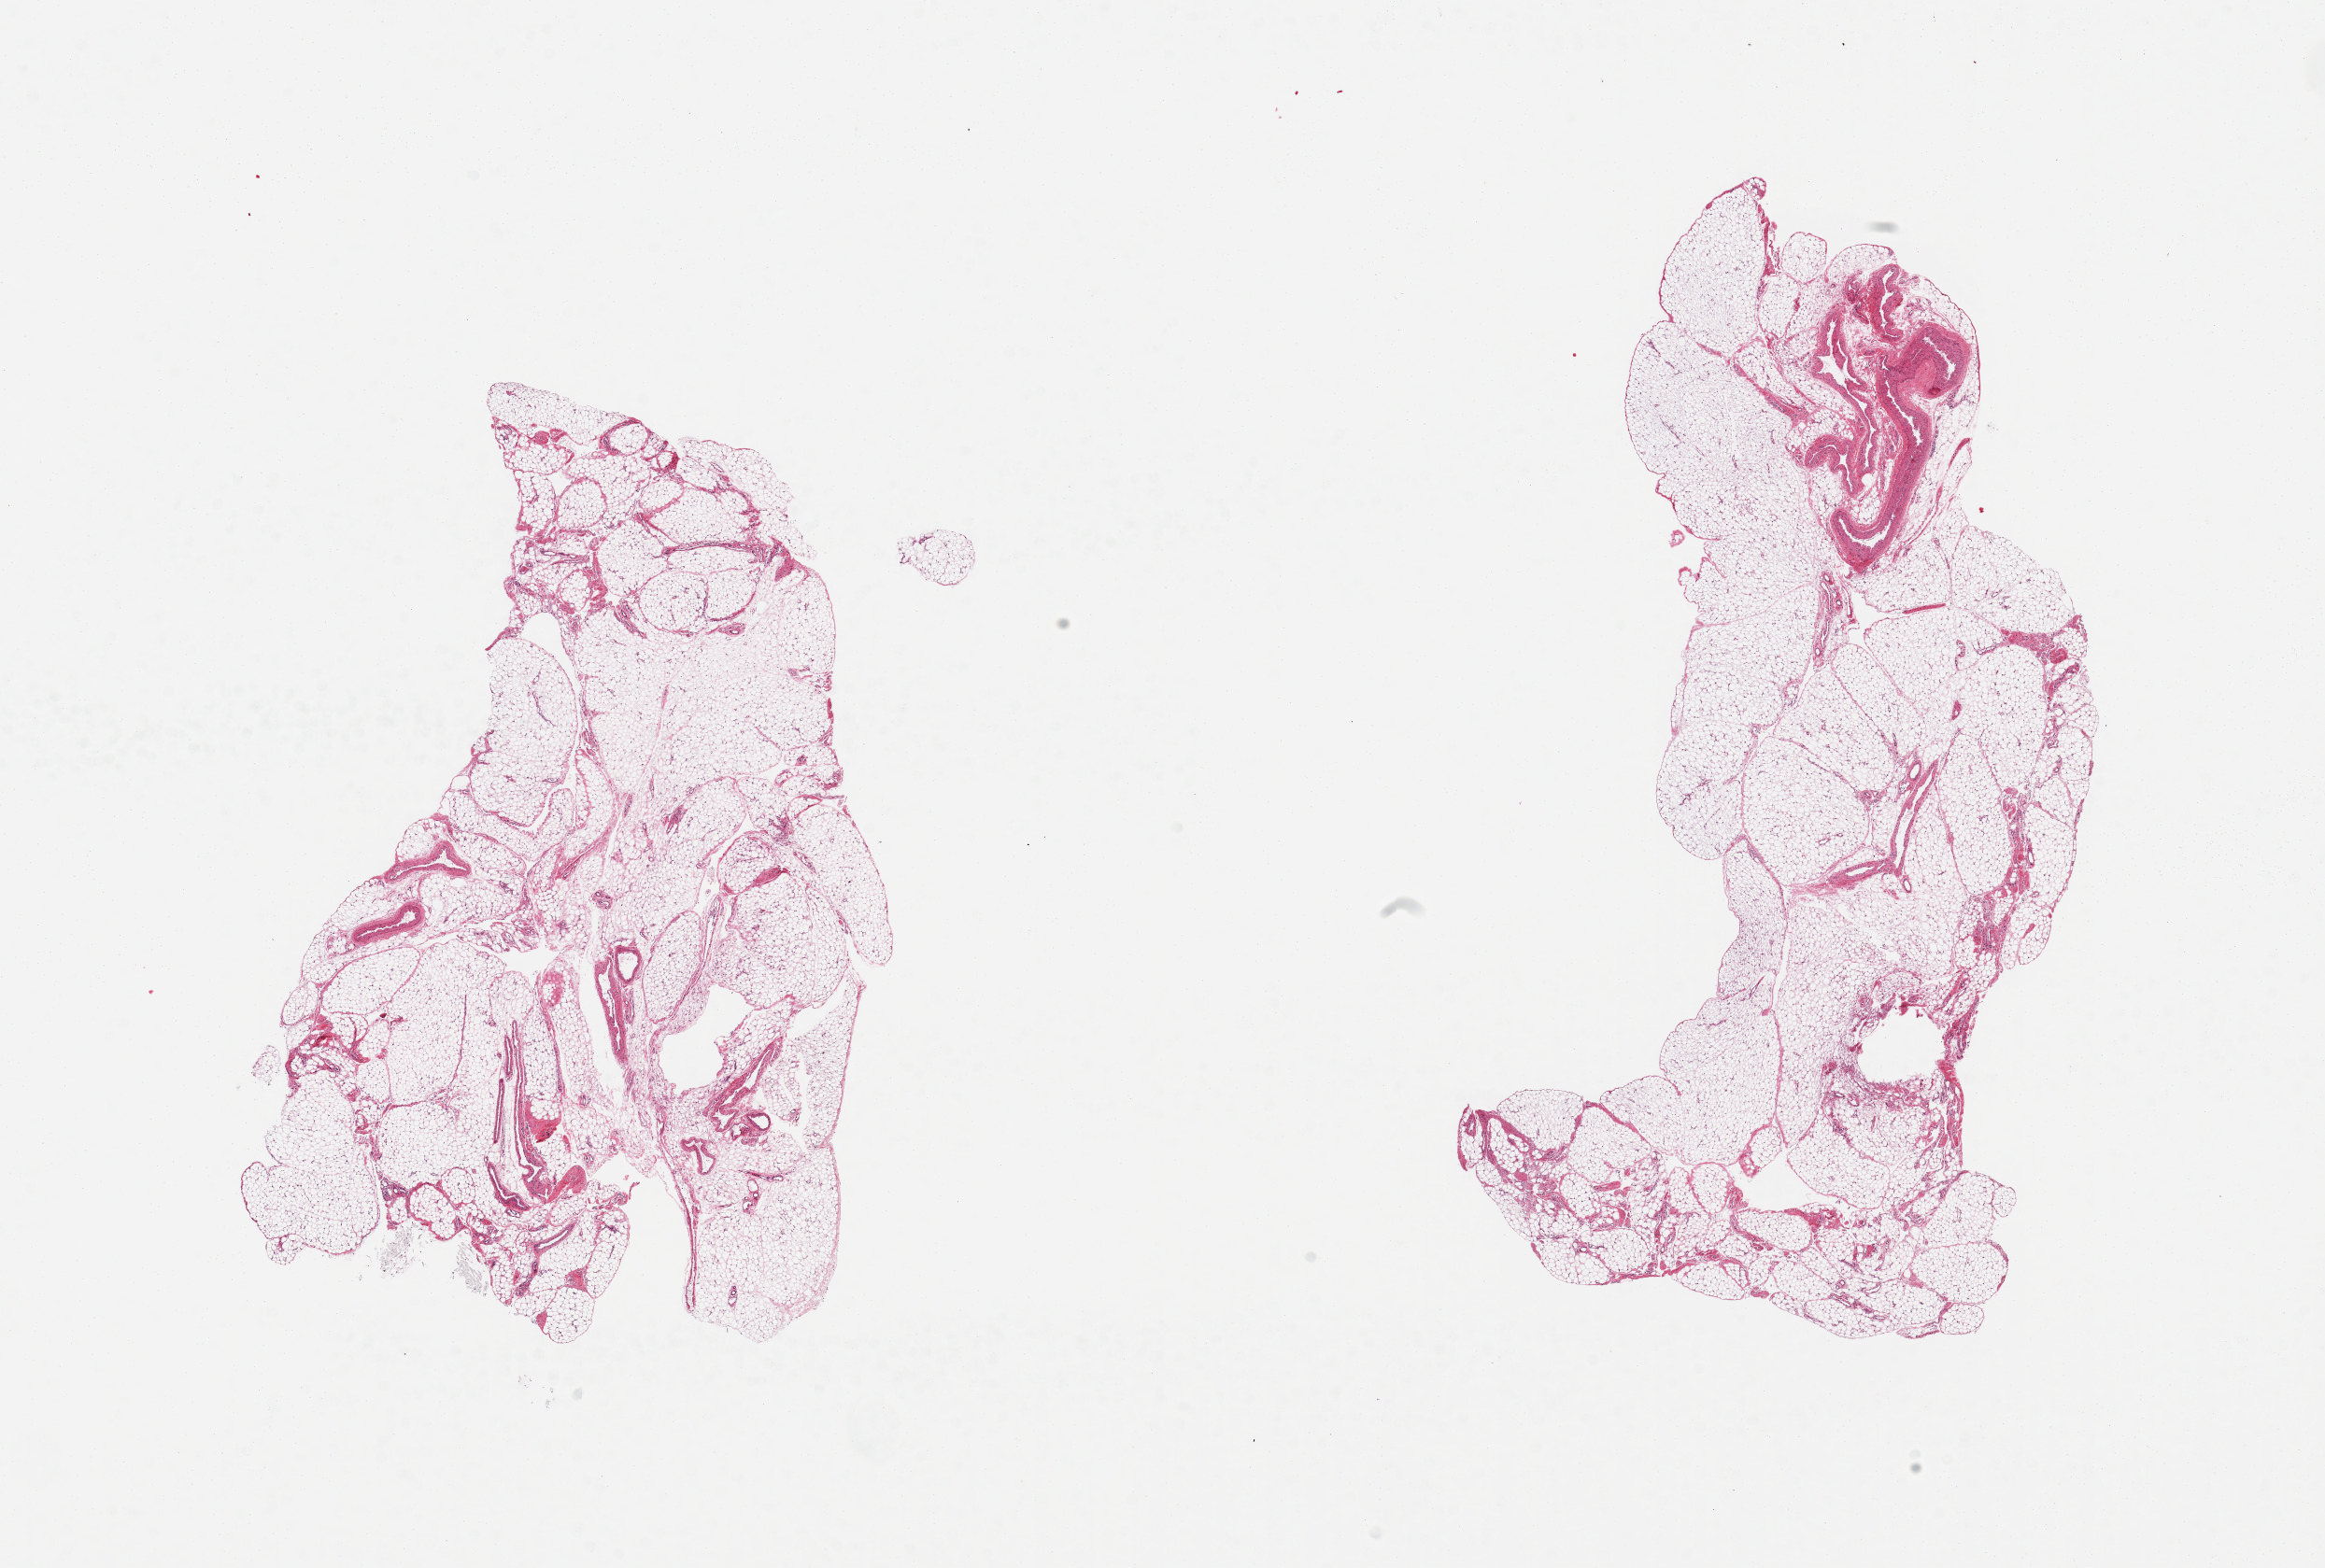
Digitized haematoxylin and eosin-stained section, brightfield — a low-resolution overview of the entire scanned area, about 19.7 x 13.3 mm (acquisition: 20x scan), PAXgene-fixed paraffin-embedded (PFPE) section, section of omentum (target tissue), tissue donor sample. Female donor.
- review note (as recorded): 2 pieces; lobulated fat, 1 piece includes a few larger vessels